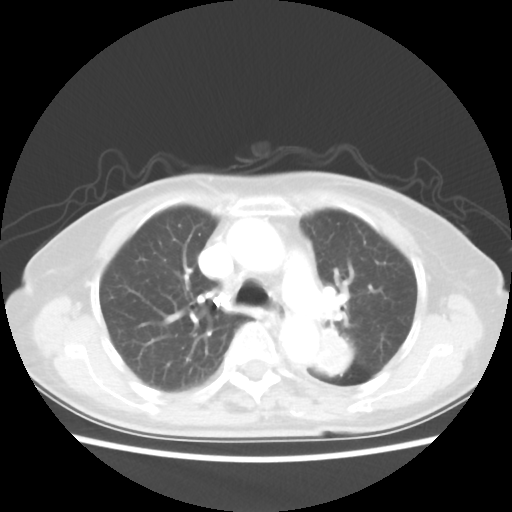
Chest CT, one axial slice; reconstruction kernel STANDARD; 80 kVp; lung window (W 1500 / L -600 HU); 512 × 512 image matrix, field of view 335 × 335 mm. Patient: female, 81 years. Case-level facts recorded for this patient, not image findings: clinical TNM (as recorded): T2 N0 M1a.
Outlined on this slice (rectangle marked by the reading radiologist):
- lung tumour (recorded histology: squamous cell carcinoma): box from (x=310, y=318) to (x=351, y=374) px